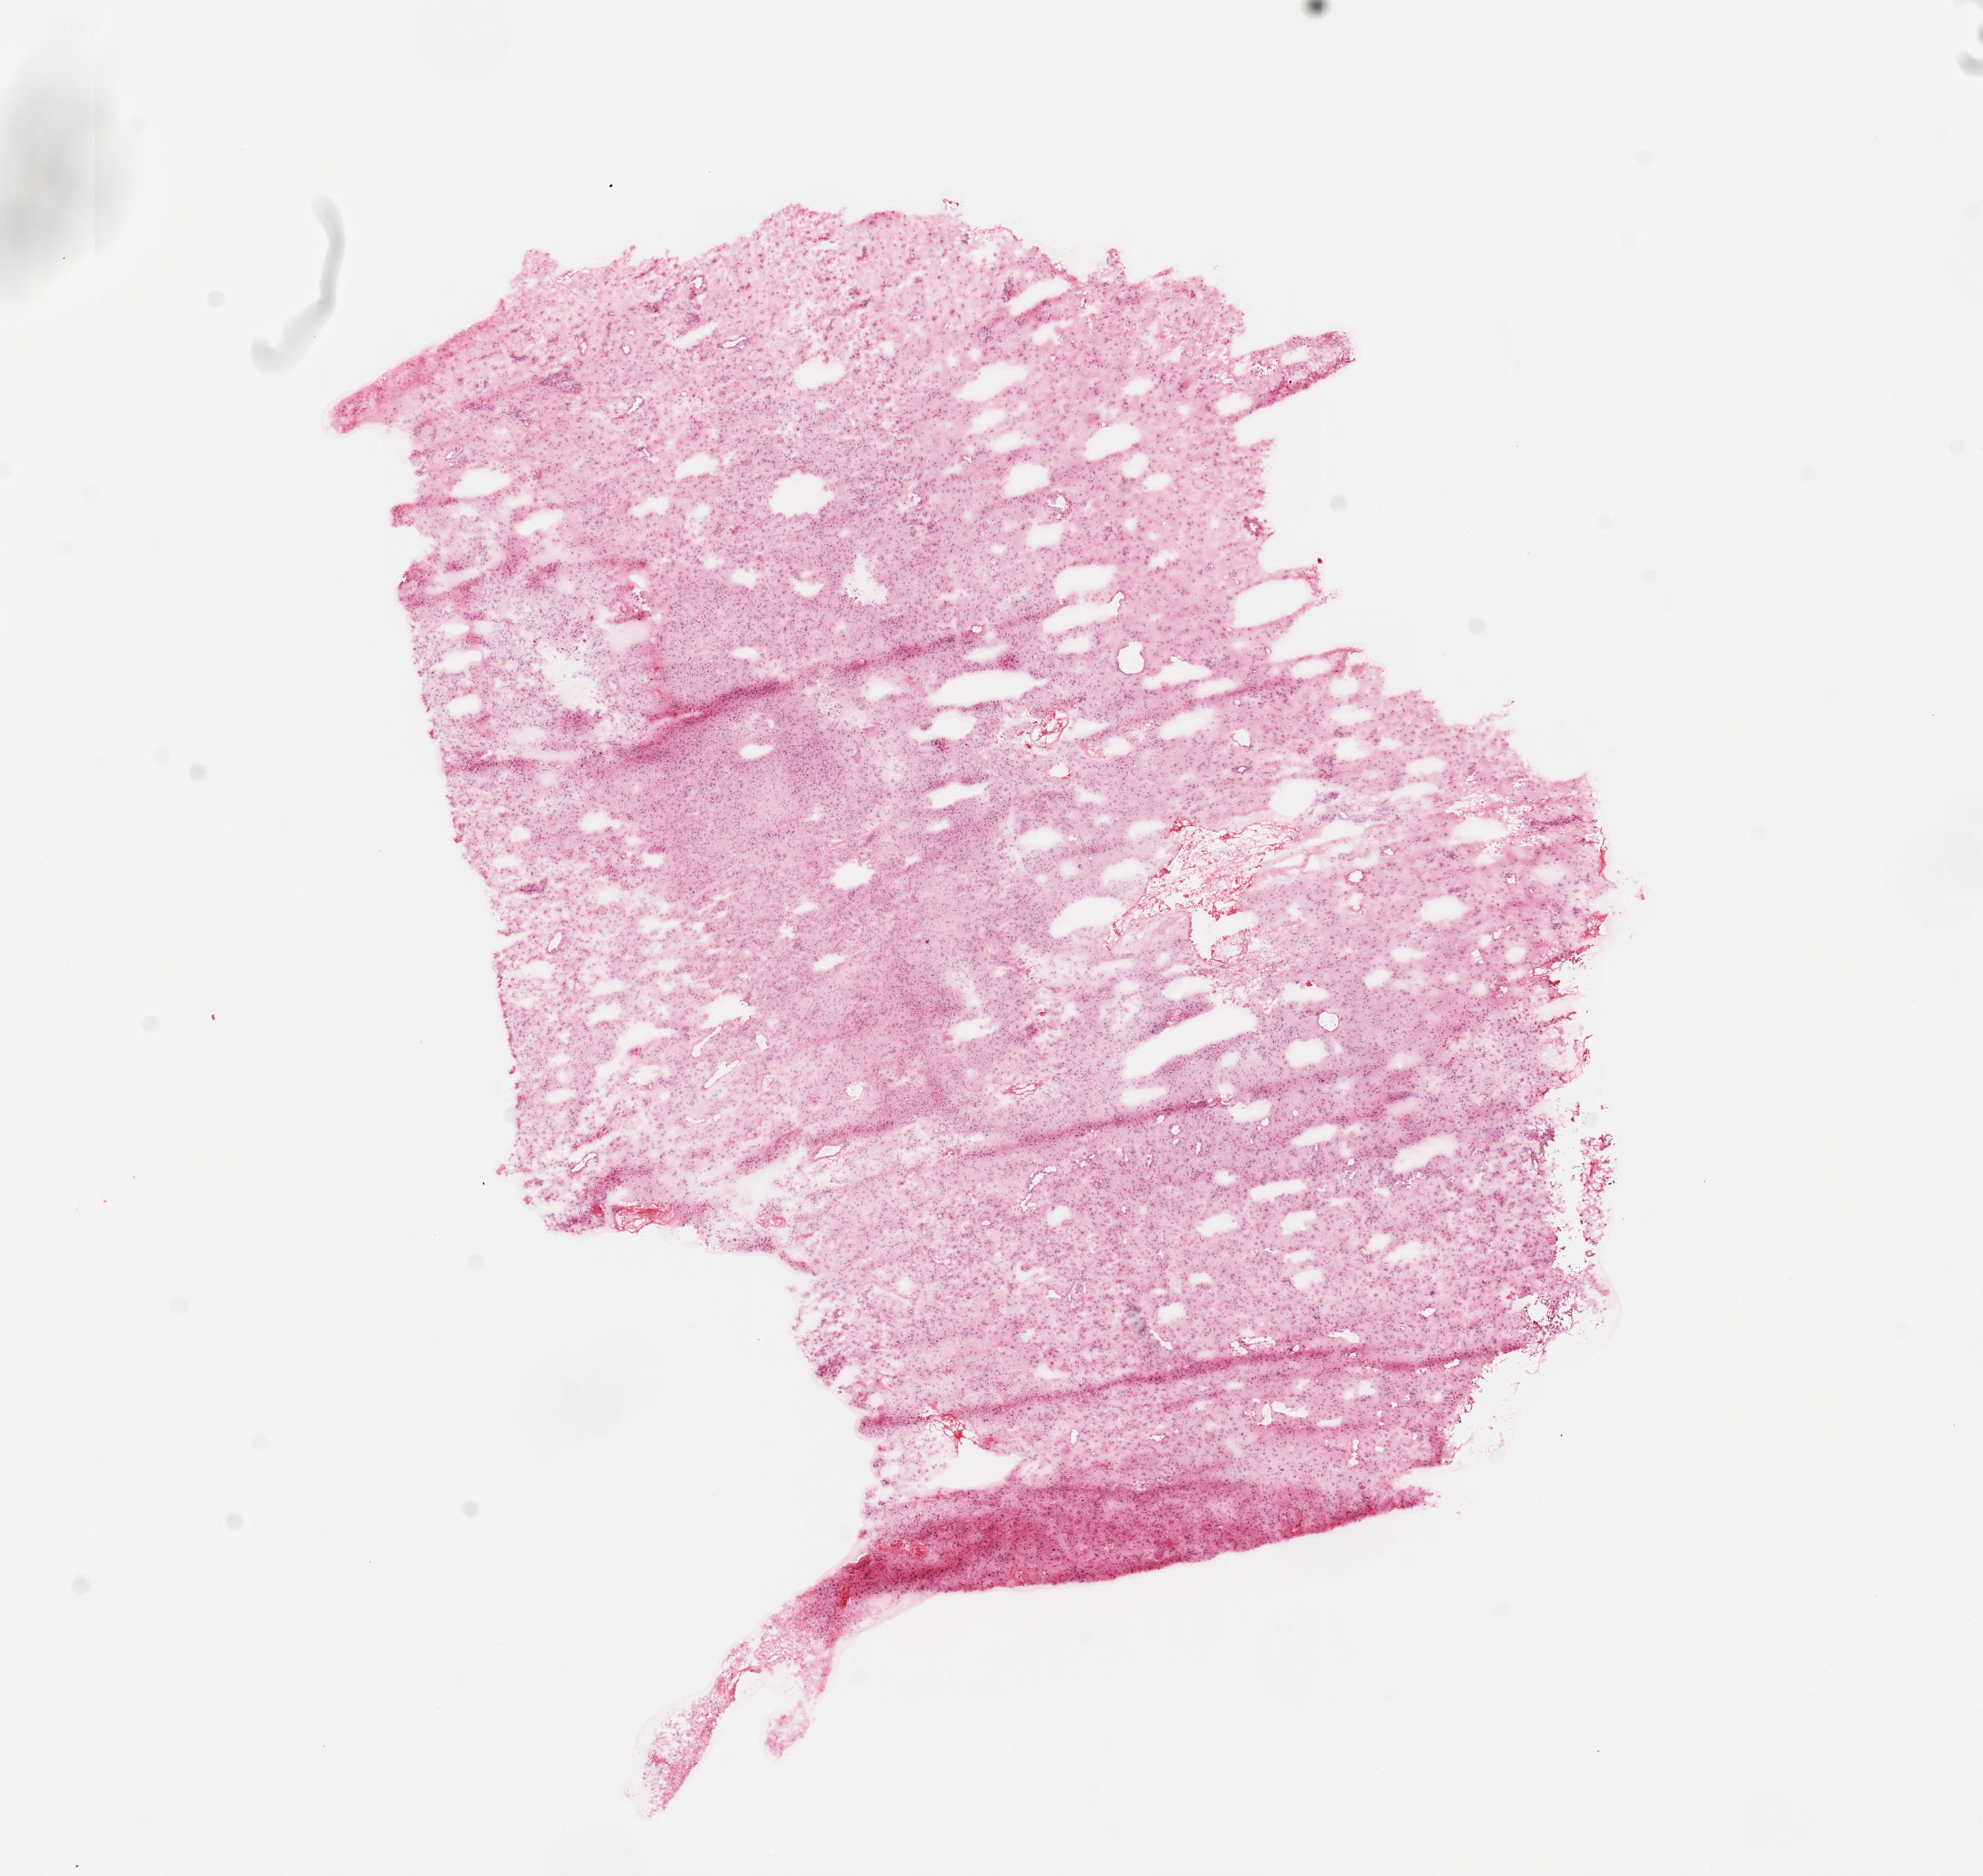
Digitized Hematoxylin and eosin (H&E) stained tissue section (whole slide), shown as a low-resolution overview of the whole scanned area (about 10.2 x 9.6 mm); frozen section; brain, primary tumour sample. Male patient; age at initial diagnosis 79 years. Composition of this section per pathologist review: tumour cells 75%, tumour nuclei 80%.
Diagnosis: Glioblastoma.